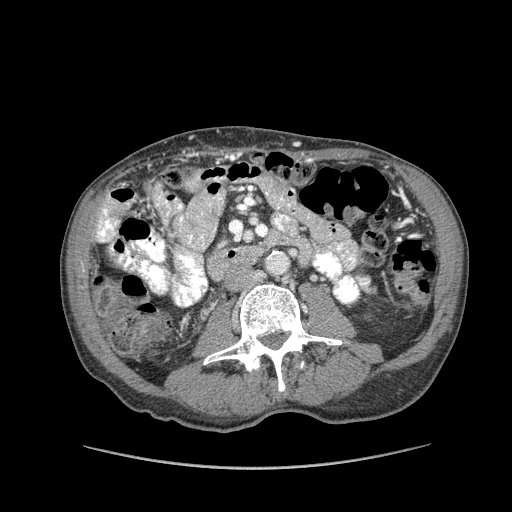
Contrast-enhanced abdominal CT (liver protocol), one axial slice. Position 3 of 162 along the scan axis. Soft-tissue window (W 400 / L 40 HU). 512 × 512 image matrix, field of view 400 × 400 mm. From the clinical record (not read from this slice): diagnosis: hepatocellular carcinoma (patient treated with transarterial chemoembolisation; whether this scan precedes or follows treatment is not stated here); TNM stage (as recorded): Stage-IIIA; Child-Pugh class: A.
Outlined on this slice (semi-automatically segmented with operator editing):
- liver parenchyma outside the tumour (the mass and vessels are separate outlines, so this box may not span the whole liver): bounding box (x1, y1, x2, y2) in pixels: (96, 204, 116, 242)
- liver vessels: (97, 209, 115, 242)